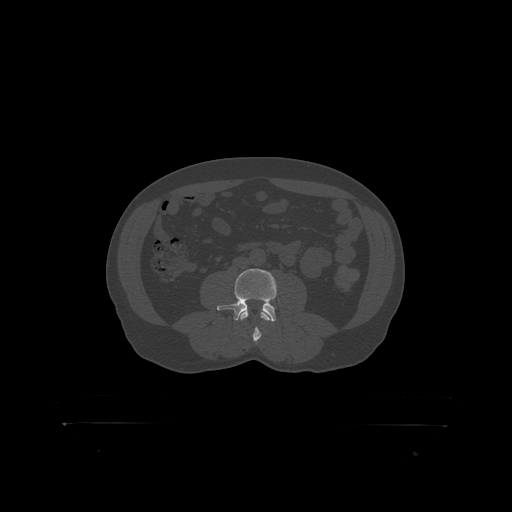
CT including the spine, one axial slice. Position 247 of 399 along the scan axis. Reconstruction kernel STANDARD. 120 kVp. Bone window (W 1800 / L 400 HU). 1.25 mm slice thickness. 512 × 512 image matrix, field of view 650 × 650 mm. Male patient, age 46 years. From the clinical record (not read from this slice): primary cancer: skin.
Outlined on this slice (semi-automatically segmented with operator editing):
- L3 vertebra: bounding box [x1, y1, x2, y2] px = [241, 311, 269, 319]
- L4 vertebra: [220, 269, 277, 318]